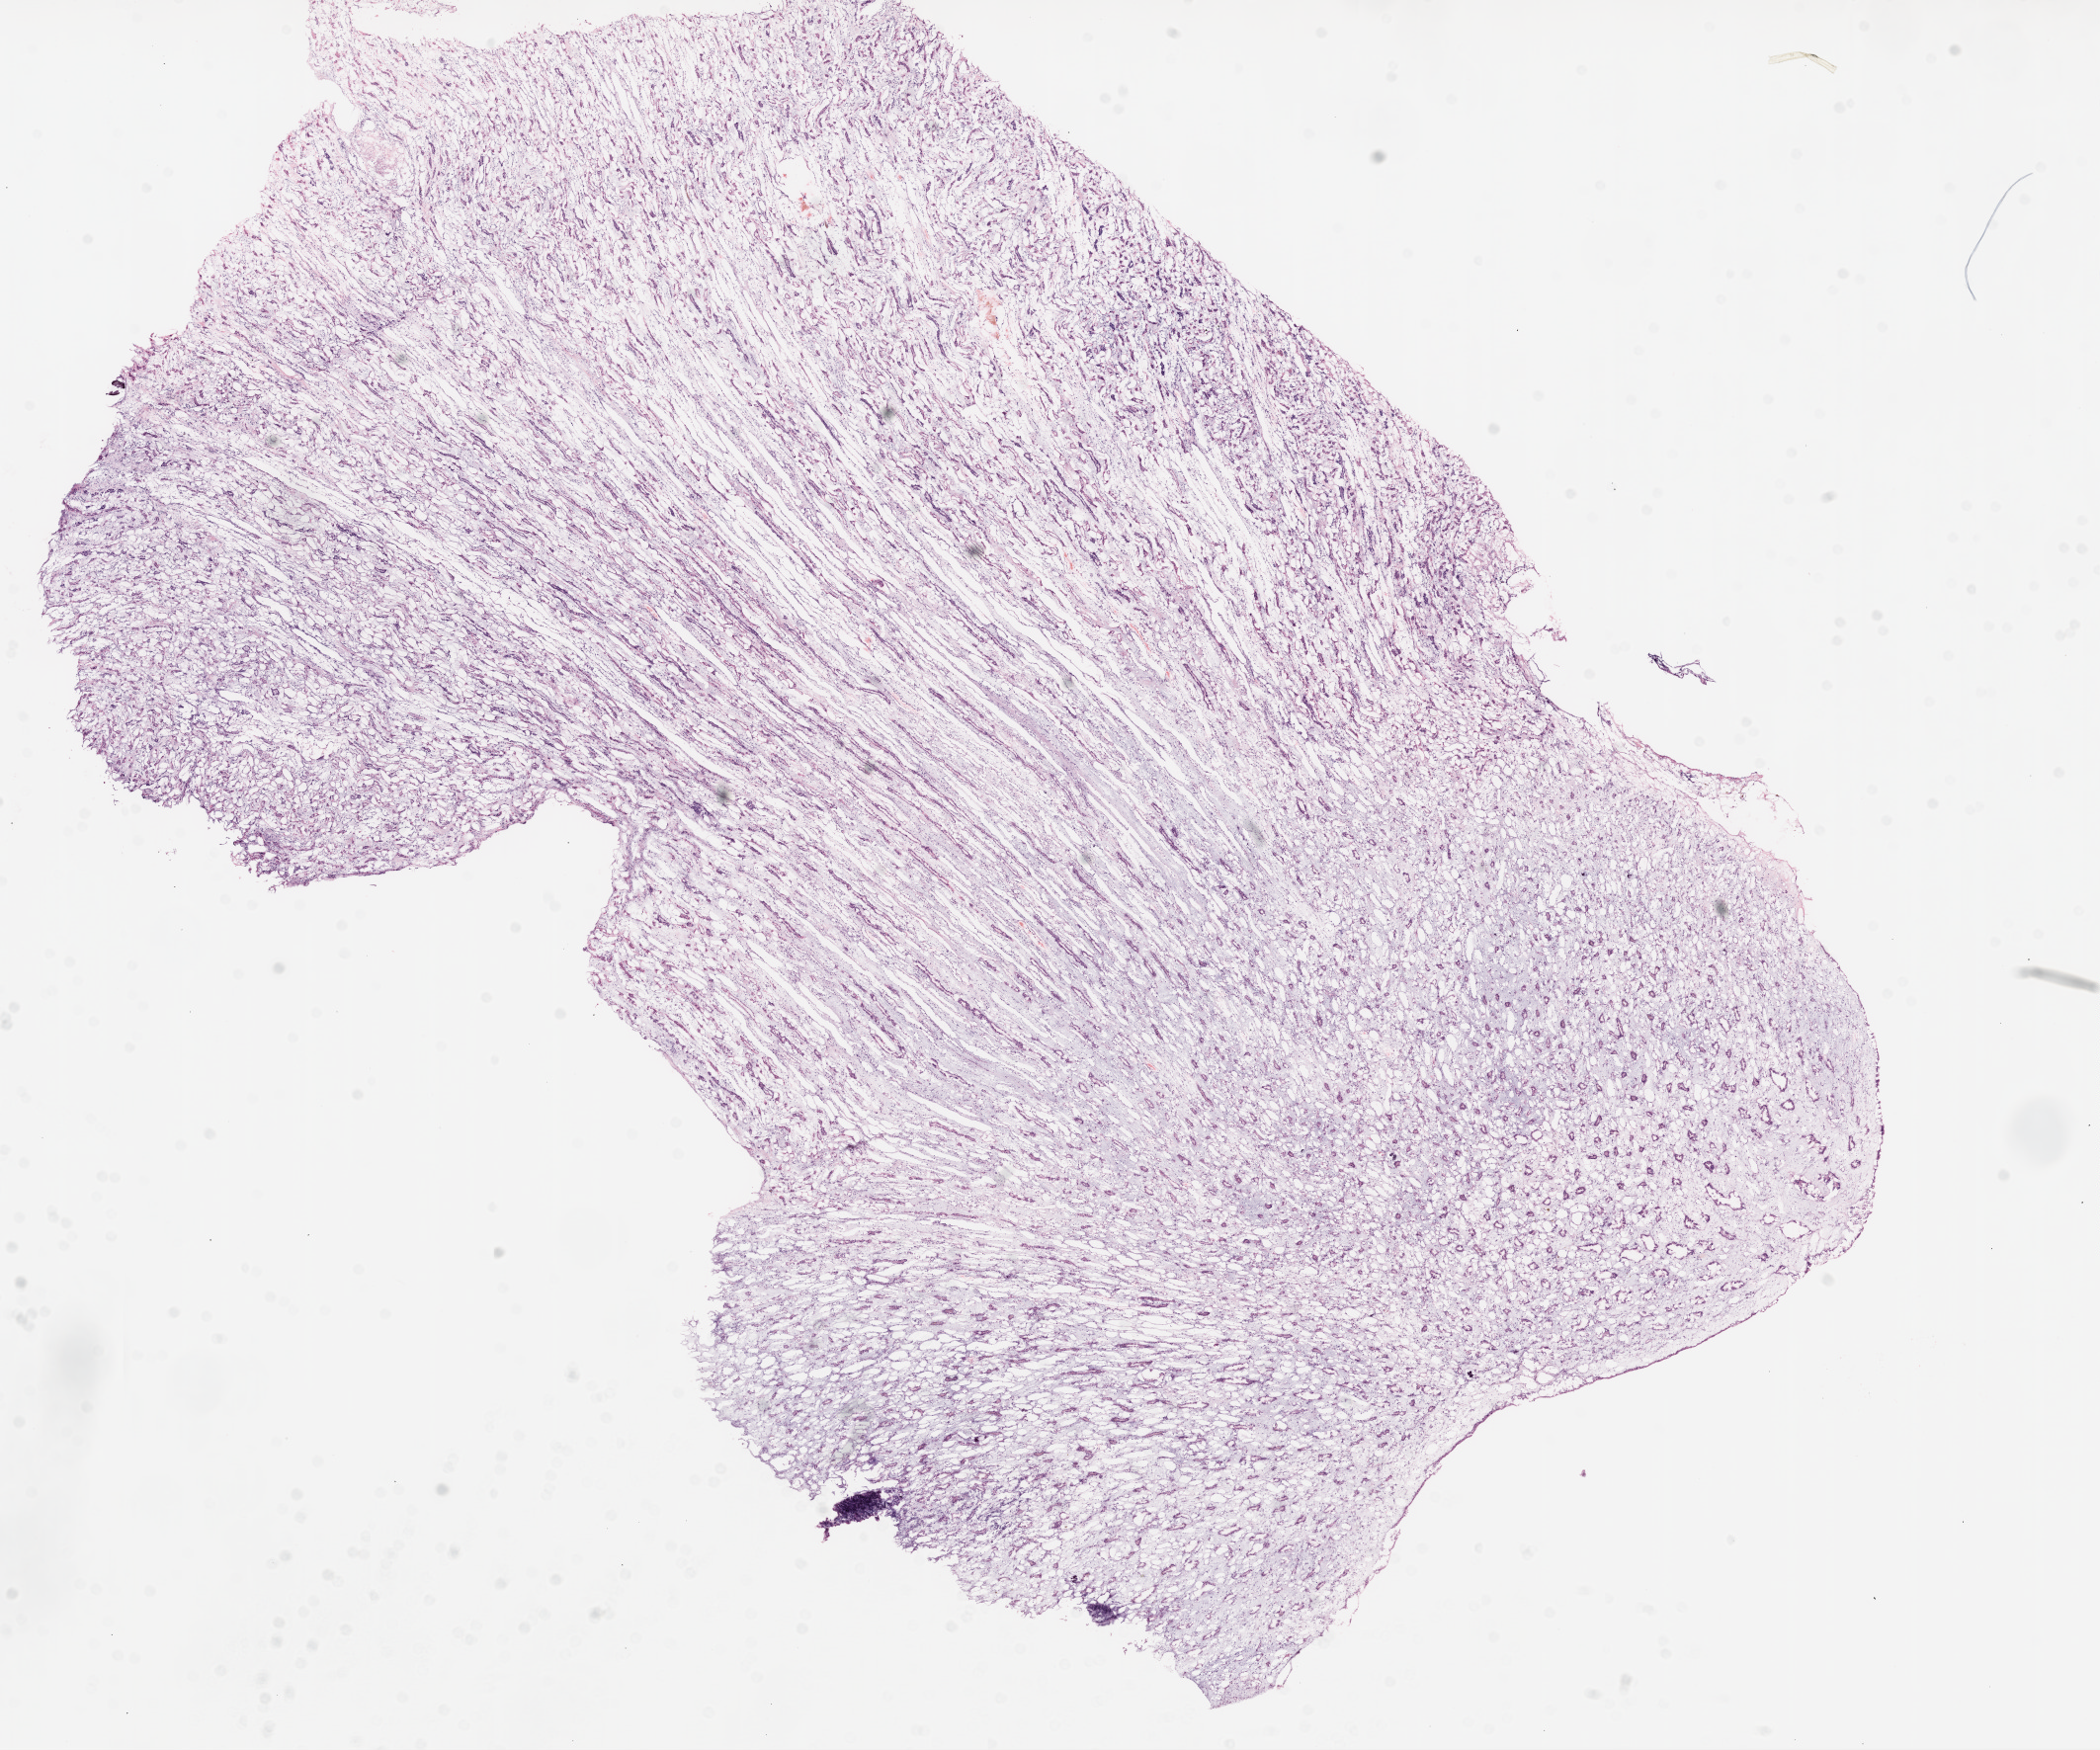
Digitized H&E-stained tissue section (whole slide), low-resolution overview of the scanned area, about 17.1 x 14.2 mm (acquisition: 20x scan); frozen section from the top of the tissue portion; sample: solid tissue normal (non-tumour tissue), kidney. Male, age 56 years at initial diagnosis.
This section: solid tissue normal (non-tumour) sample from the same patient. Patient diagnosis: Clear cell adenocarcinoma, NOS.